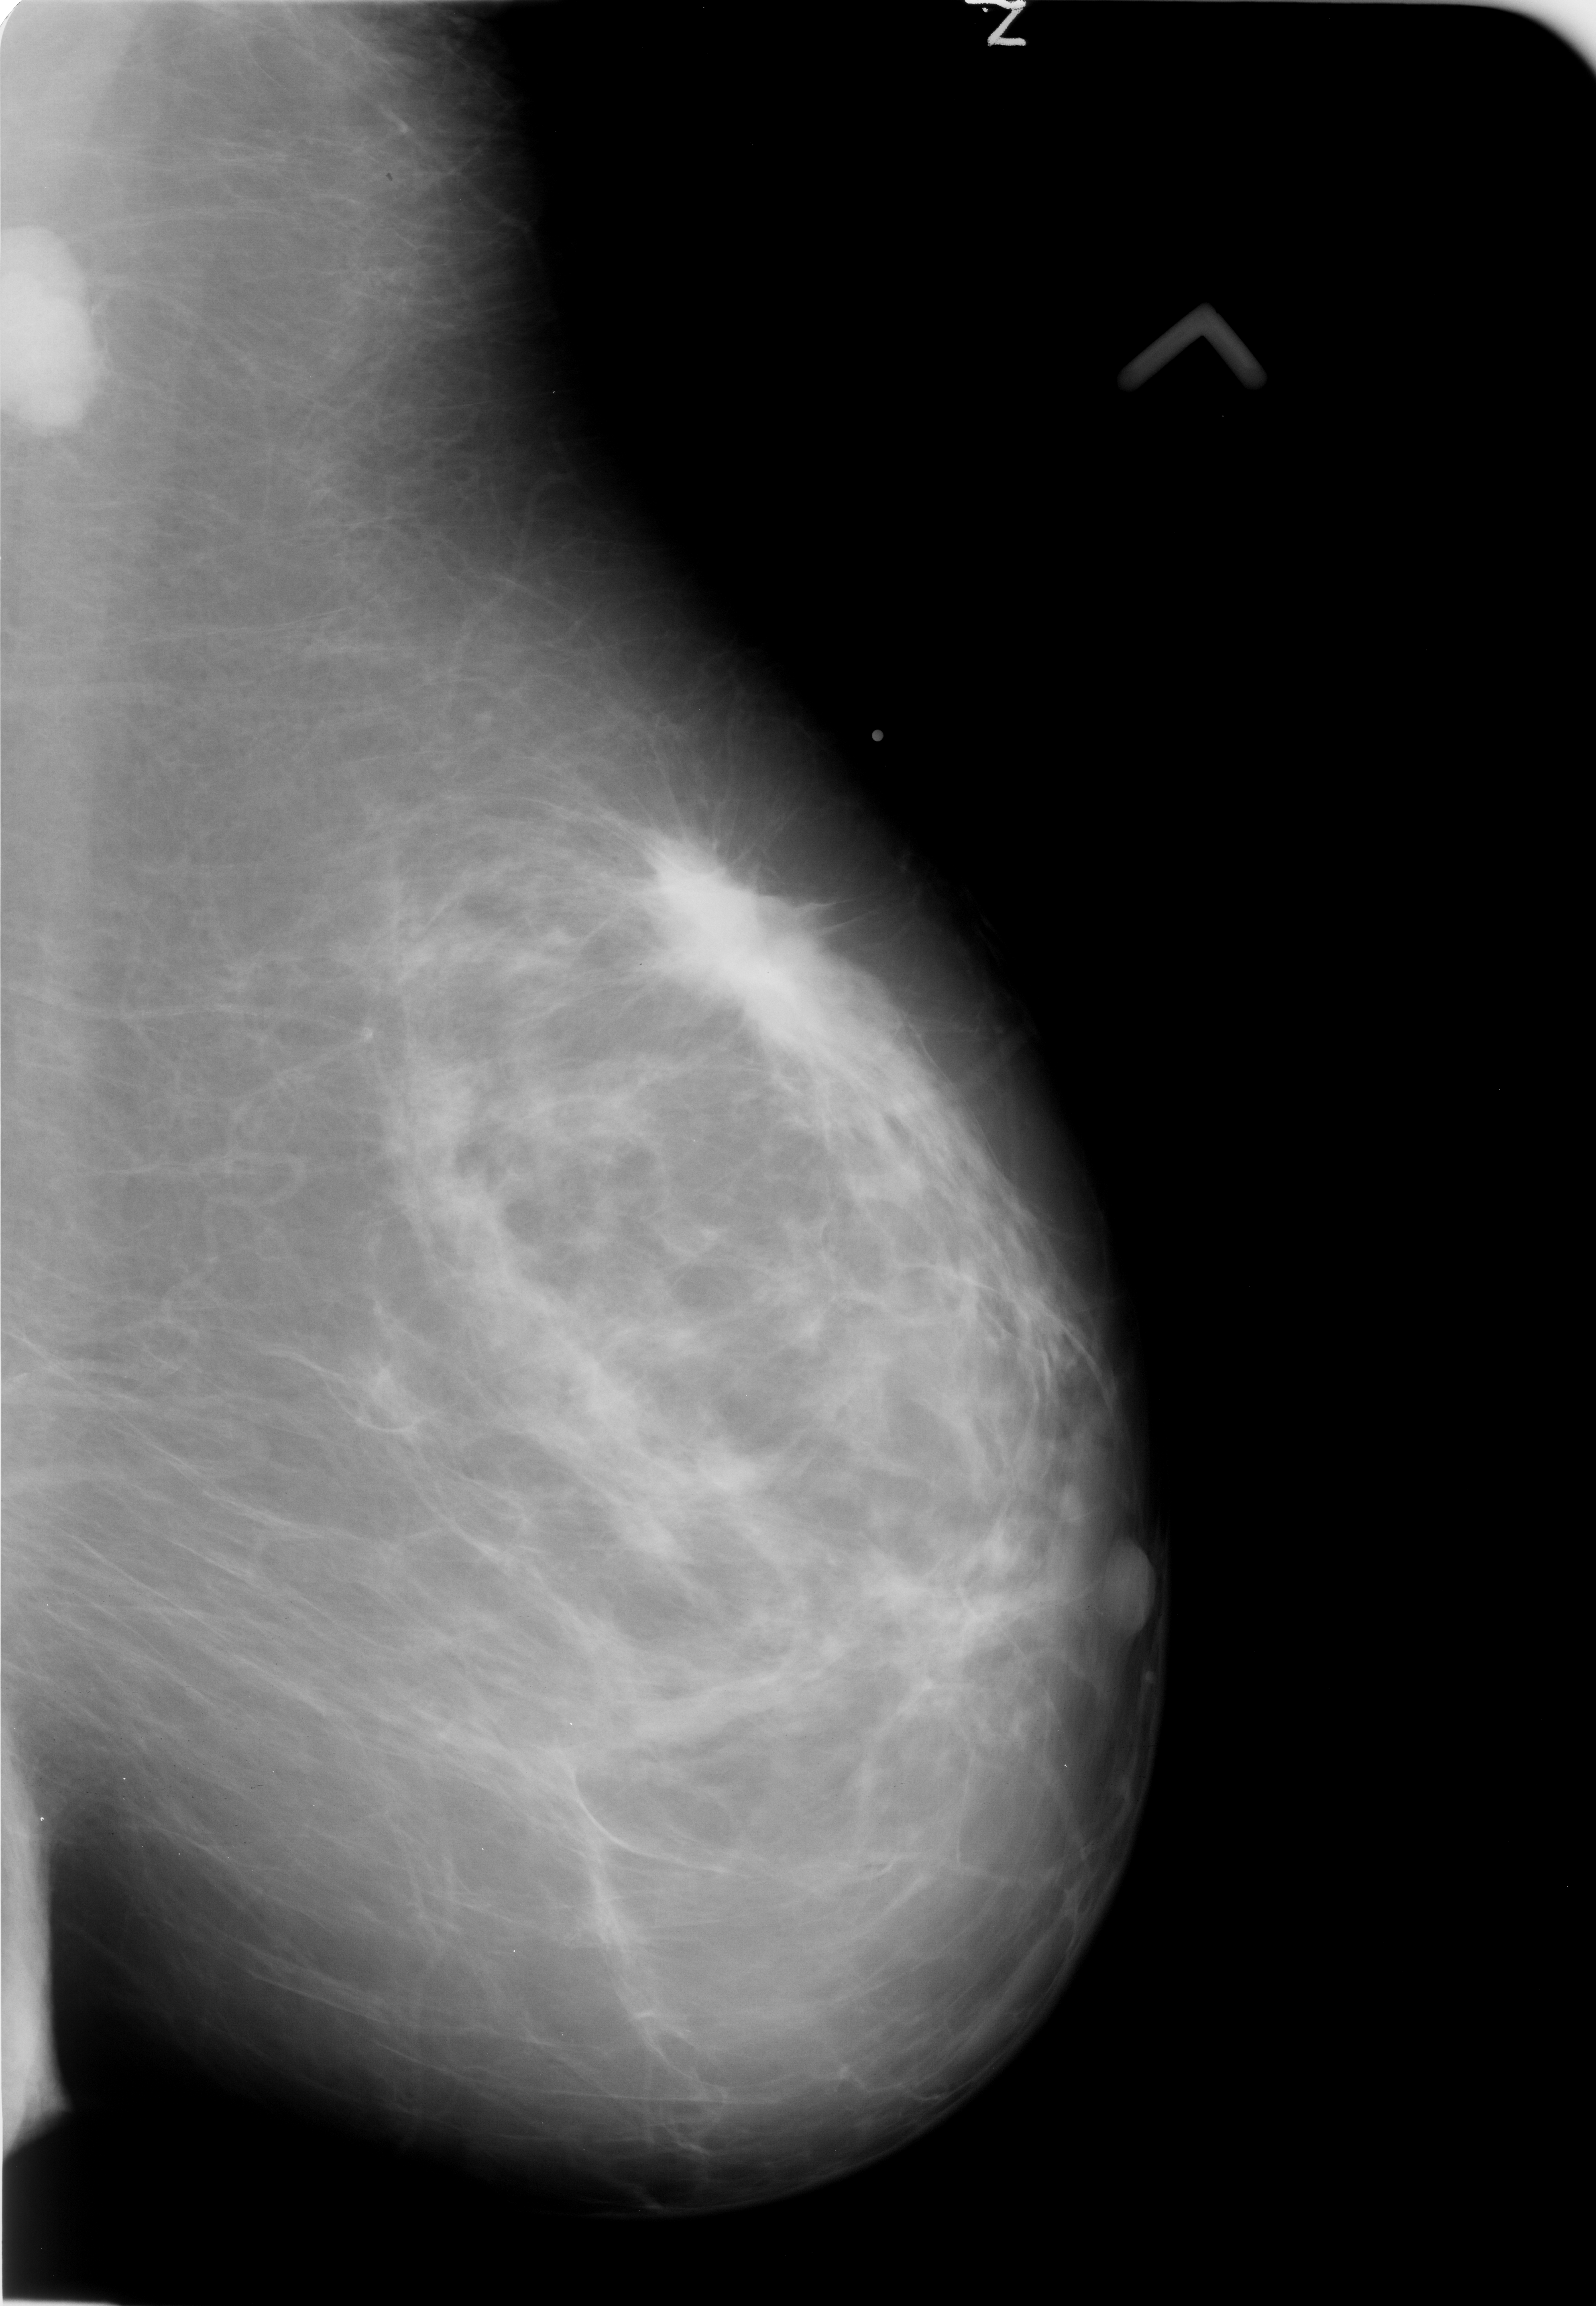
Scanned film-screen mammogram; left breast; MLO view; breast composition: scattered fibroglandular densities (BI-RADS density category 2 of 4).
- Abnormality record for this image: mass, shape irregular / architectural distortion, margins spiculated; BI-RADS assessment category 5; subtlety rating 5 on a 1 (subtle) to 5 (obvious) scale; pathology (as recorded): malignant.